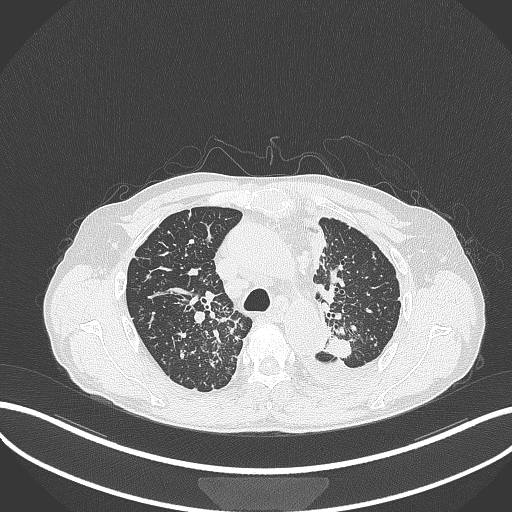
Chest CT, one axial slice; position 254 of 325 along the scan axis; reconstruction kernel B70f; lung window (W 1500 / L -600 HU); 512 × 512 image matrix, field of view 400 × 400 mm. Patient: male, 58 years. From the clinical record (not read from this slice): clinical TNM (as recorded): T1c N3 M1.
Structures marked on this image (rectangle marked by the reading radiologist):
- lung tumour (recorded histology: adenocarcinoma): bounding box [x1, y1, x2, y2] px = [318, 333, 354, 361]